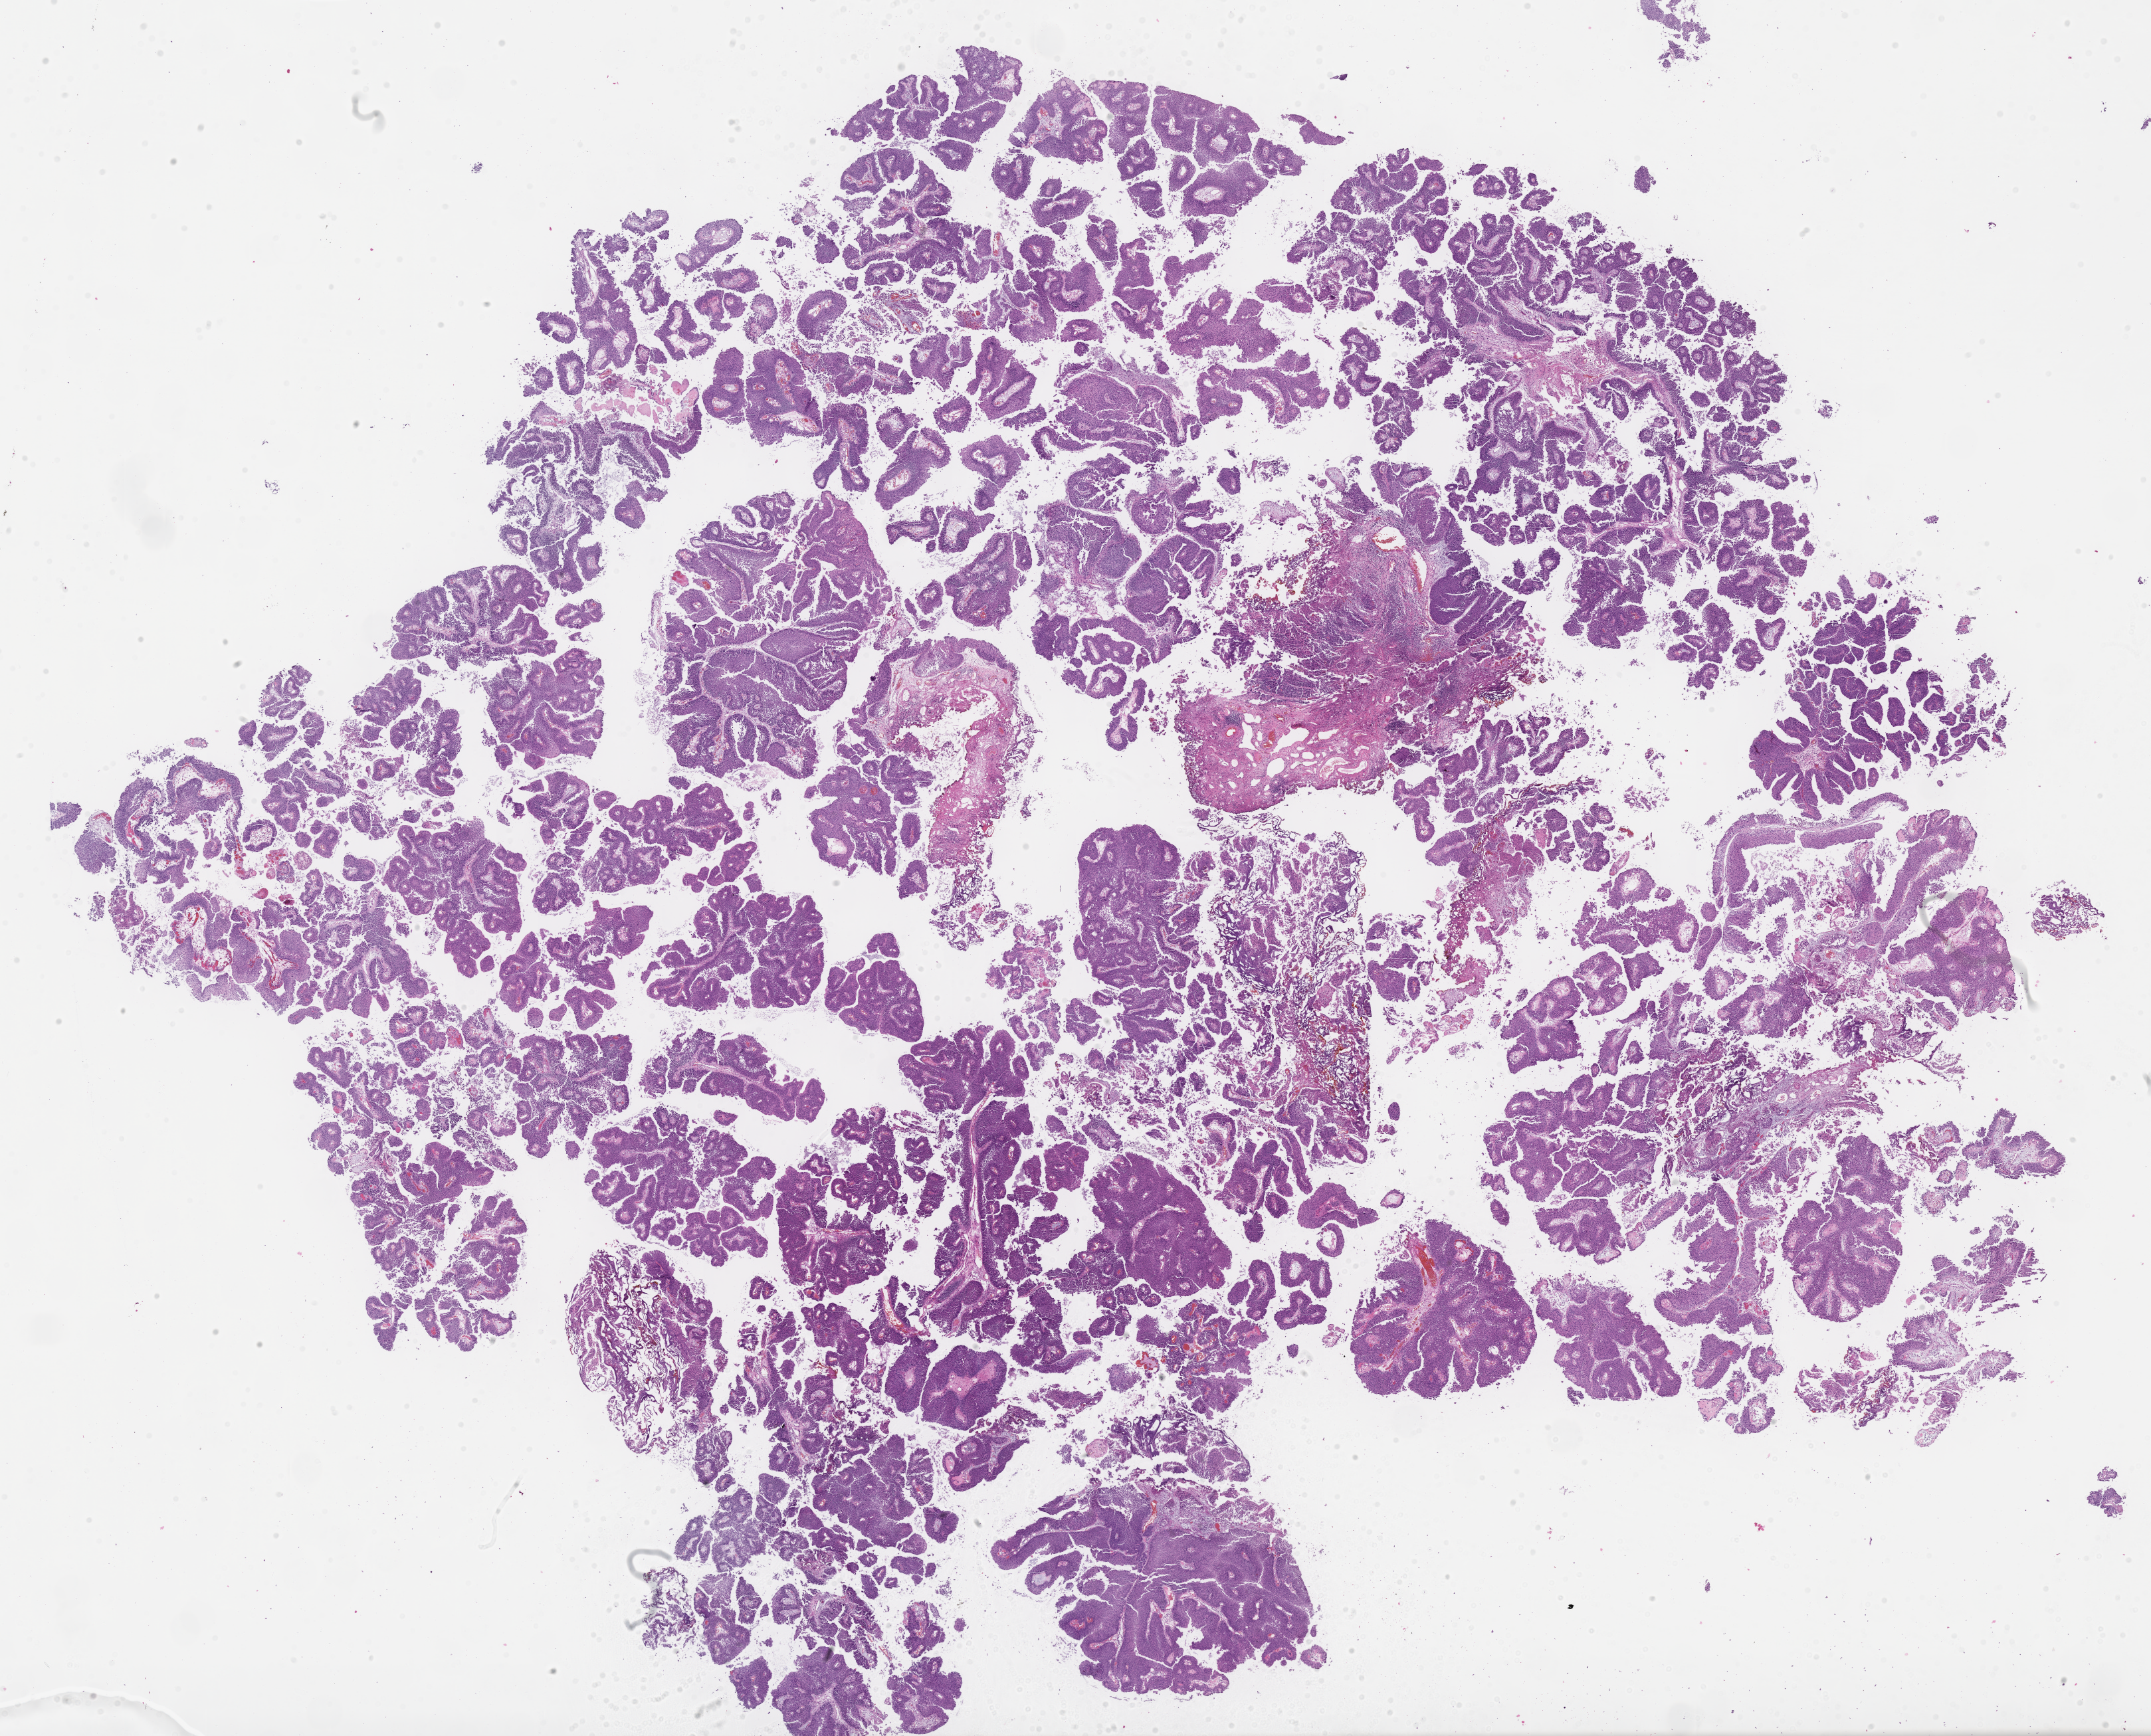
Whole-slide image, haematoxylin and eosin stain — whole scanned area (about 26.1 x 21.1 mm) shown as a low-resolution overview, formalin-fixed, paraffin-embedded (FFPE) tissue, specimen: primary tumor, site: lateral wall of bladder. Patient: female. Slide review estimates, as recorded: tumor cells 80%, tumor nuclei 90%, stromal cells 18%, necrosis 0%, normal cells 2%. Inflammatory infiltration, as recorded: lymphocyte infiltration 0%, monocyte infiltration 0%, neutrophil infiltration 0%.
• section: bottom of the tissue portion
• diagnosis: Papillary urothelial carcinoma